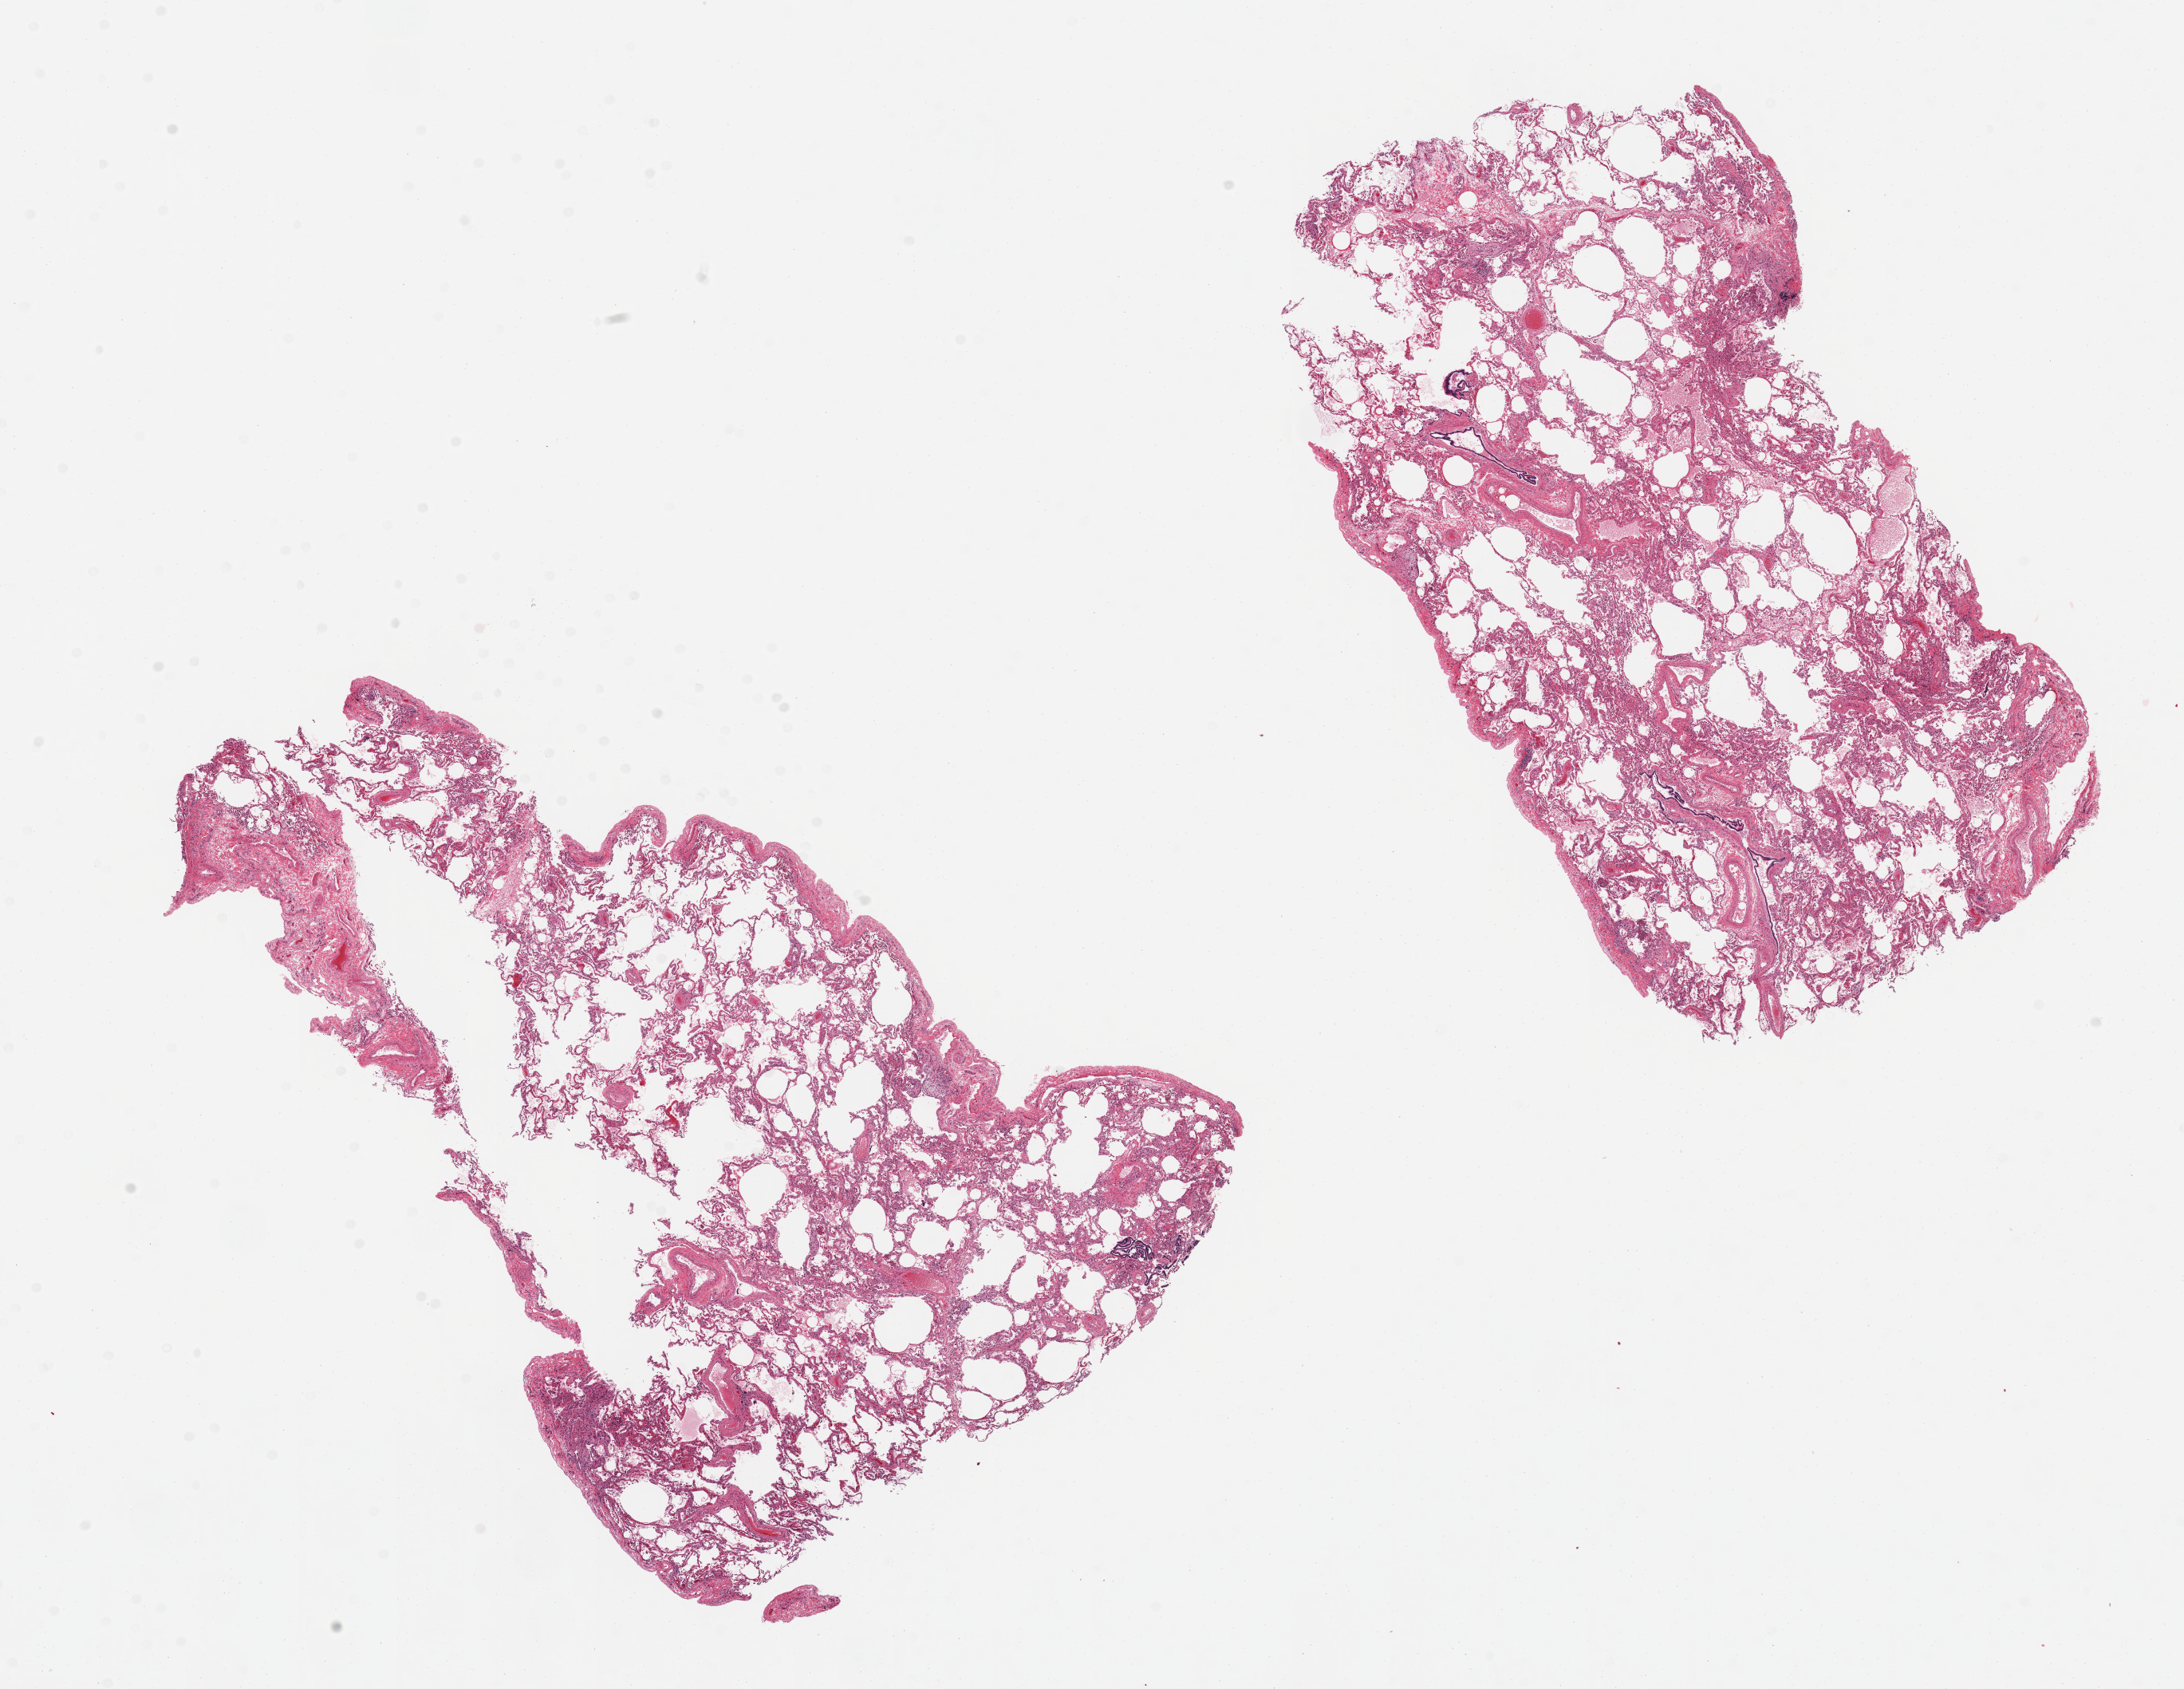
Haematoxylin and eosin whole-slide image — a low-resolution overview of the entire scanned area, about 21.7 x 16.7 mm, PAXgene-fixed, paraffin-embedded tissue, section of lung (target tissue), donor tissue sample.
Pathologist's review note for this sample: 2 pieces, emphysema.